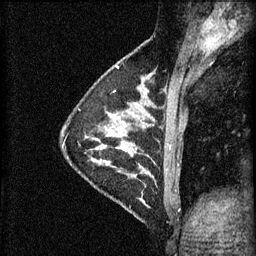
Breast MRI (dynamic contrast-enhanced), one sagittal slice; slice 20 of 60 in the series (ordered by position); 3 images stored at this slice position (order not interpretable as contrast timing); 1.5 T; TE 4.2 ms, TR 11 ms; 2 mm slice thickness; 256 × 256 image matrix, field of view 180 × 180 mm. Female patient, age 29 years.
Outlined on this slice (semi-automatic segmentation, software-assisted and operator-edited):
- analysis volume of interest (the breast-tissue region the enhancement analysis was run in; not a lesion): box from (x=106, y=172) to (x=171, y=225) px
- tumour enhancement mask (voxels above the 70 % enhancement threshold inside the analysis volume of interest): (x=143, y=172)–(x=151, y=203)